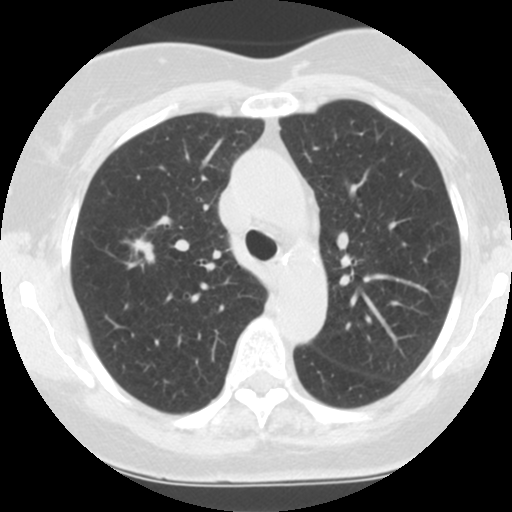
Axial slice from a low-dose chest CT screening exam; third screening round (two years after baseline); lung window (W 1500 / L -600 HU); 2.5 mm slice thickness; slice 150 of 212 in the series; 512 × 512 image matrix. Female participant, aged 62 years at enrolment. Former smoker at enrolment.
Lesion marked by an expert reader, bounding box <109,226,168,276> (left, top, right, bottom; pixels). The exam's reader record, not a measurement of the box and not confirmed to be the same lesion: non-calcified nodule or mass ≥4 mm, right upper lobe, 14 × 9 mm, spiculated (stellate) margins, soft tissue attenuation, pre-existing on the prior screen: yes; interval growth: yes.